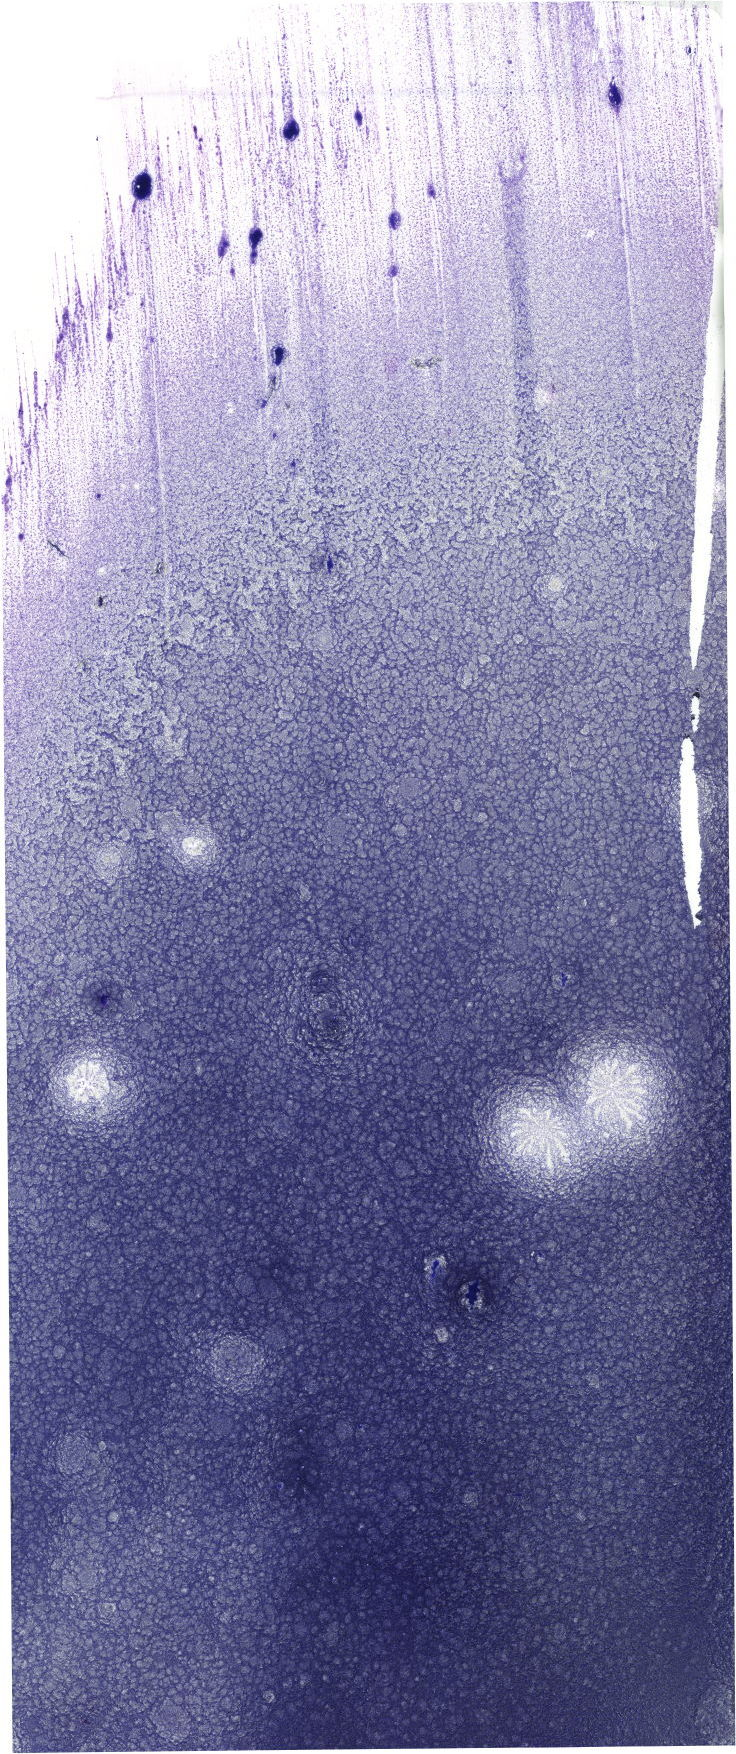
May-Grünwald–Giemsa-stained marrow aspirate smear (whole slide) — low-resolution overview of the scanned area, about 20.9 x 49.7 mm. Patient sex: male.
Diagnosis: Chronic Phase Chronic Myeloid Leukemia, BCR-ABL1 Positive.